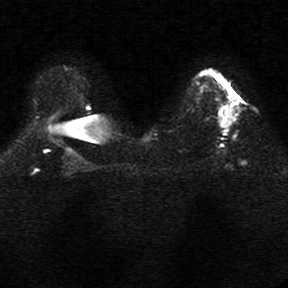
Breast MRI, one axial slice. Position 18 of 34 along the scan axis. Diffusion-weighted series; image 2 of 4 stored at this slice position (different b-values; order by instance number). 1.5 T. 288 × 288 image matrix, field of view 340 × 340 mm. Female patient.
Annotated regions visible in this slice (manually delineated by an expert):
- tumour on diffusion-weighted imaging: bounding box (x1, y1, x2, y2) in pixels: (224, 114, 231, 129)